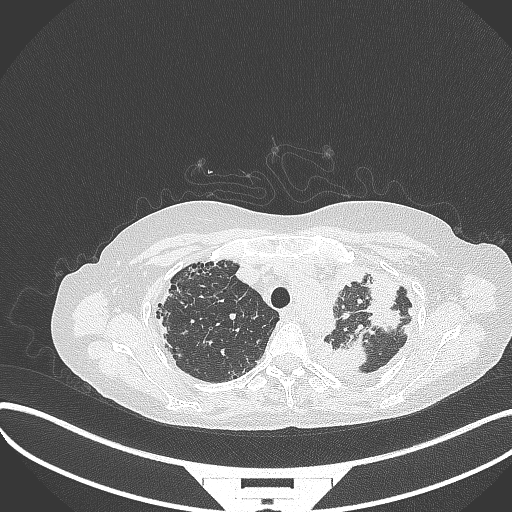
Chest CT, one axial slice. Lung window (W 1500 / L -600 HU). 1 mm slice thickness. 512 × 512 image matrix, field of view 400 × 400 mm. Patient: female, 56 years. From the clinical record (not read from this slice): clinical TNM (as recorded): T1 N0 M0.
Annotated regions visible in this slice (bounding box drawn by a radiologist):
- lung tumour (recorded histology: adenocarcinoma): bounding box (x1, y1, x2, y2) in pixels: (329, 333, 368, 373)
- lung tumour (recorded histology: adenocarcinoma): (366, 275, 410, 336)